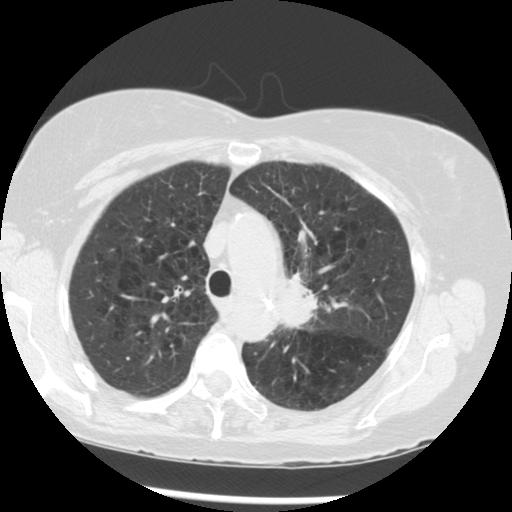
Low-dose screening chest CT, axial slice; third screening round (two years after baseline); lung window (W 1500 / L -600 HU); 2.5 mm slice thickness; standard (soft-tissue) reconstruction kernel (STANDARD); 120 kVp; 512 × 512 image matrix, field of view 330 × 330 mm. Female, age 70 years at enrolment. Current smoker at enrolment.
- Lesion marked by an expert reader, box from (x=269, y=263) to (x=362, y=353) px.
- Reader record for this screening exam (exam-level; its link to the box is not recorded): non-calcified nodule or mass ≥4 mm, left upper lobe, 32 × 26 mm, spiculated (stellate) margins, soft tissue attenuation, pre-existing on the prior screen: yes; interval growth: yes.
- Official screen result: positive, other.
- Participant outcome: lung cancer diagnosed 24 days after this screen — neoplasm, malignant, left upper lobe, stage IIIB (AJCC 6th edition), 40 mm at pathology.